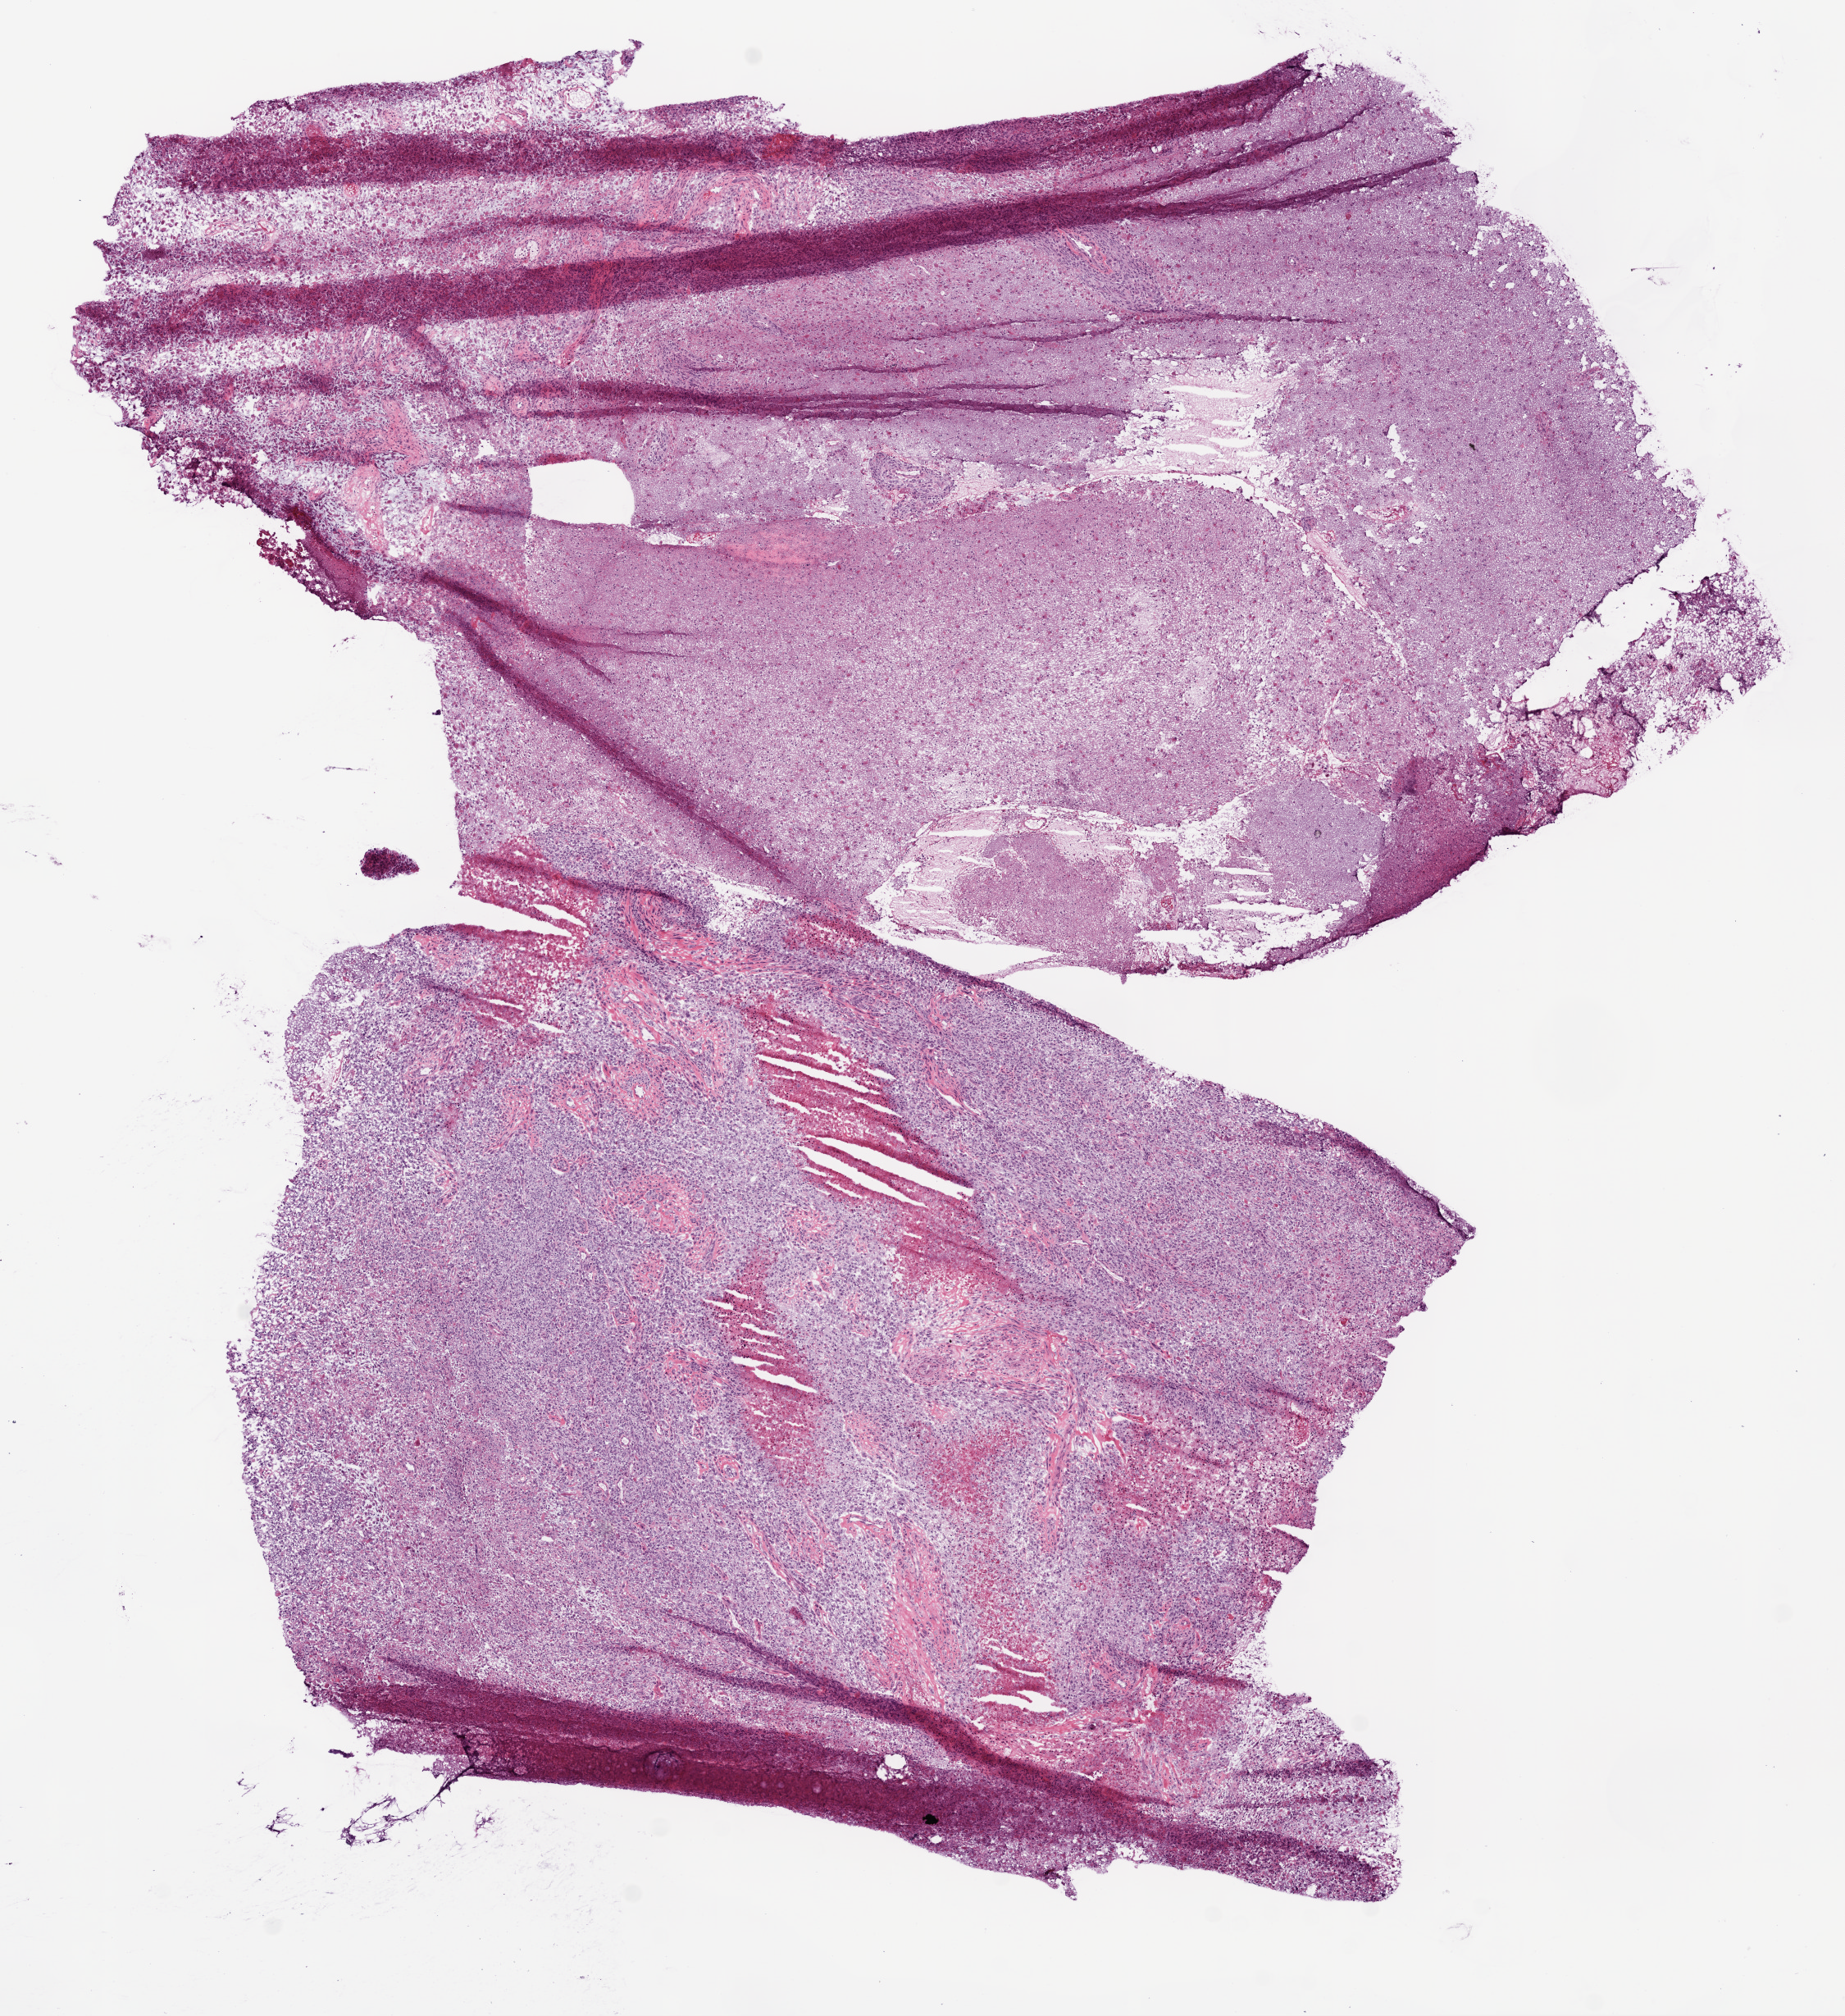
H&E whole-slide image — whole scanned area (about 9.0 x 9.9 mm) shown as a low-resolution overview; frozen section from the bottom of the tissue portion; sample: primary tumour, brain. Female patient; age at initial diagnosis 63 years. Slide review estimates, as recorded: tumour cells 95%, tumour nuclei 80%, normal cells 0%, stromal cells 0%, necrosis 10%.
- pathologic diagnosis: Glioblastoma